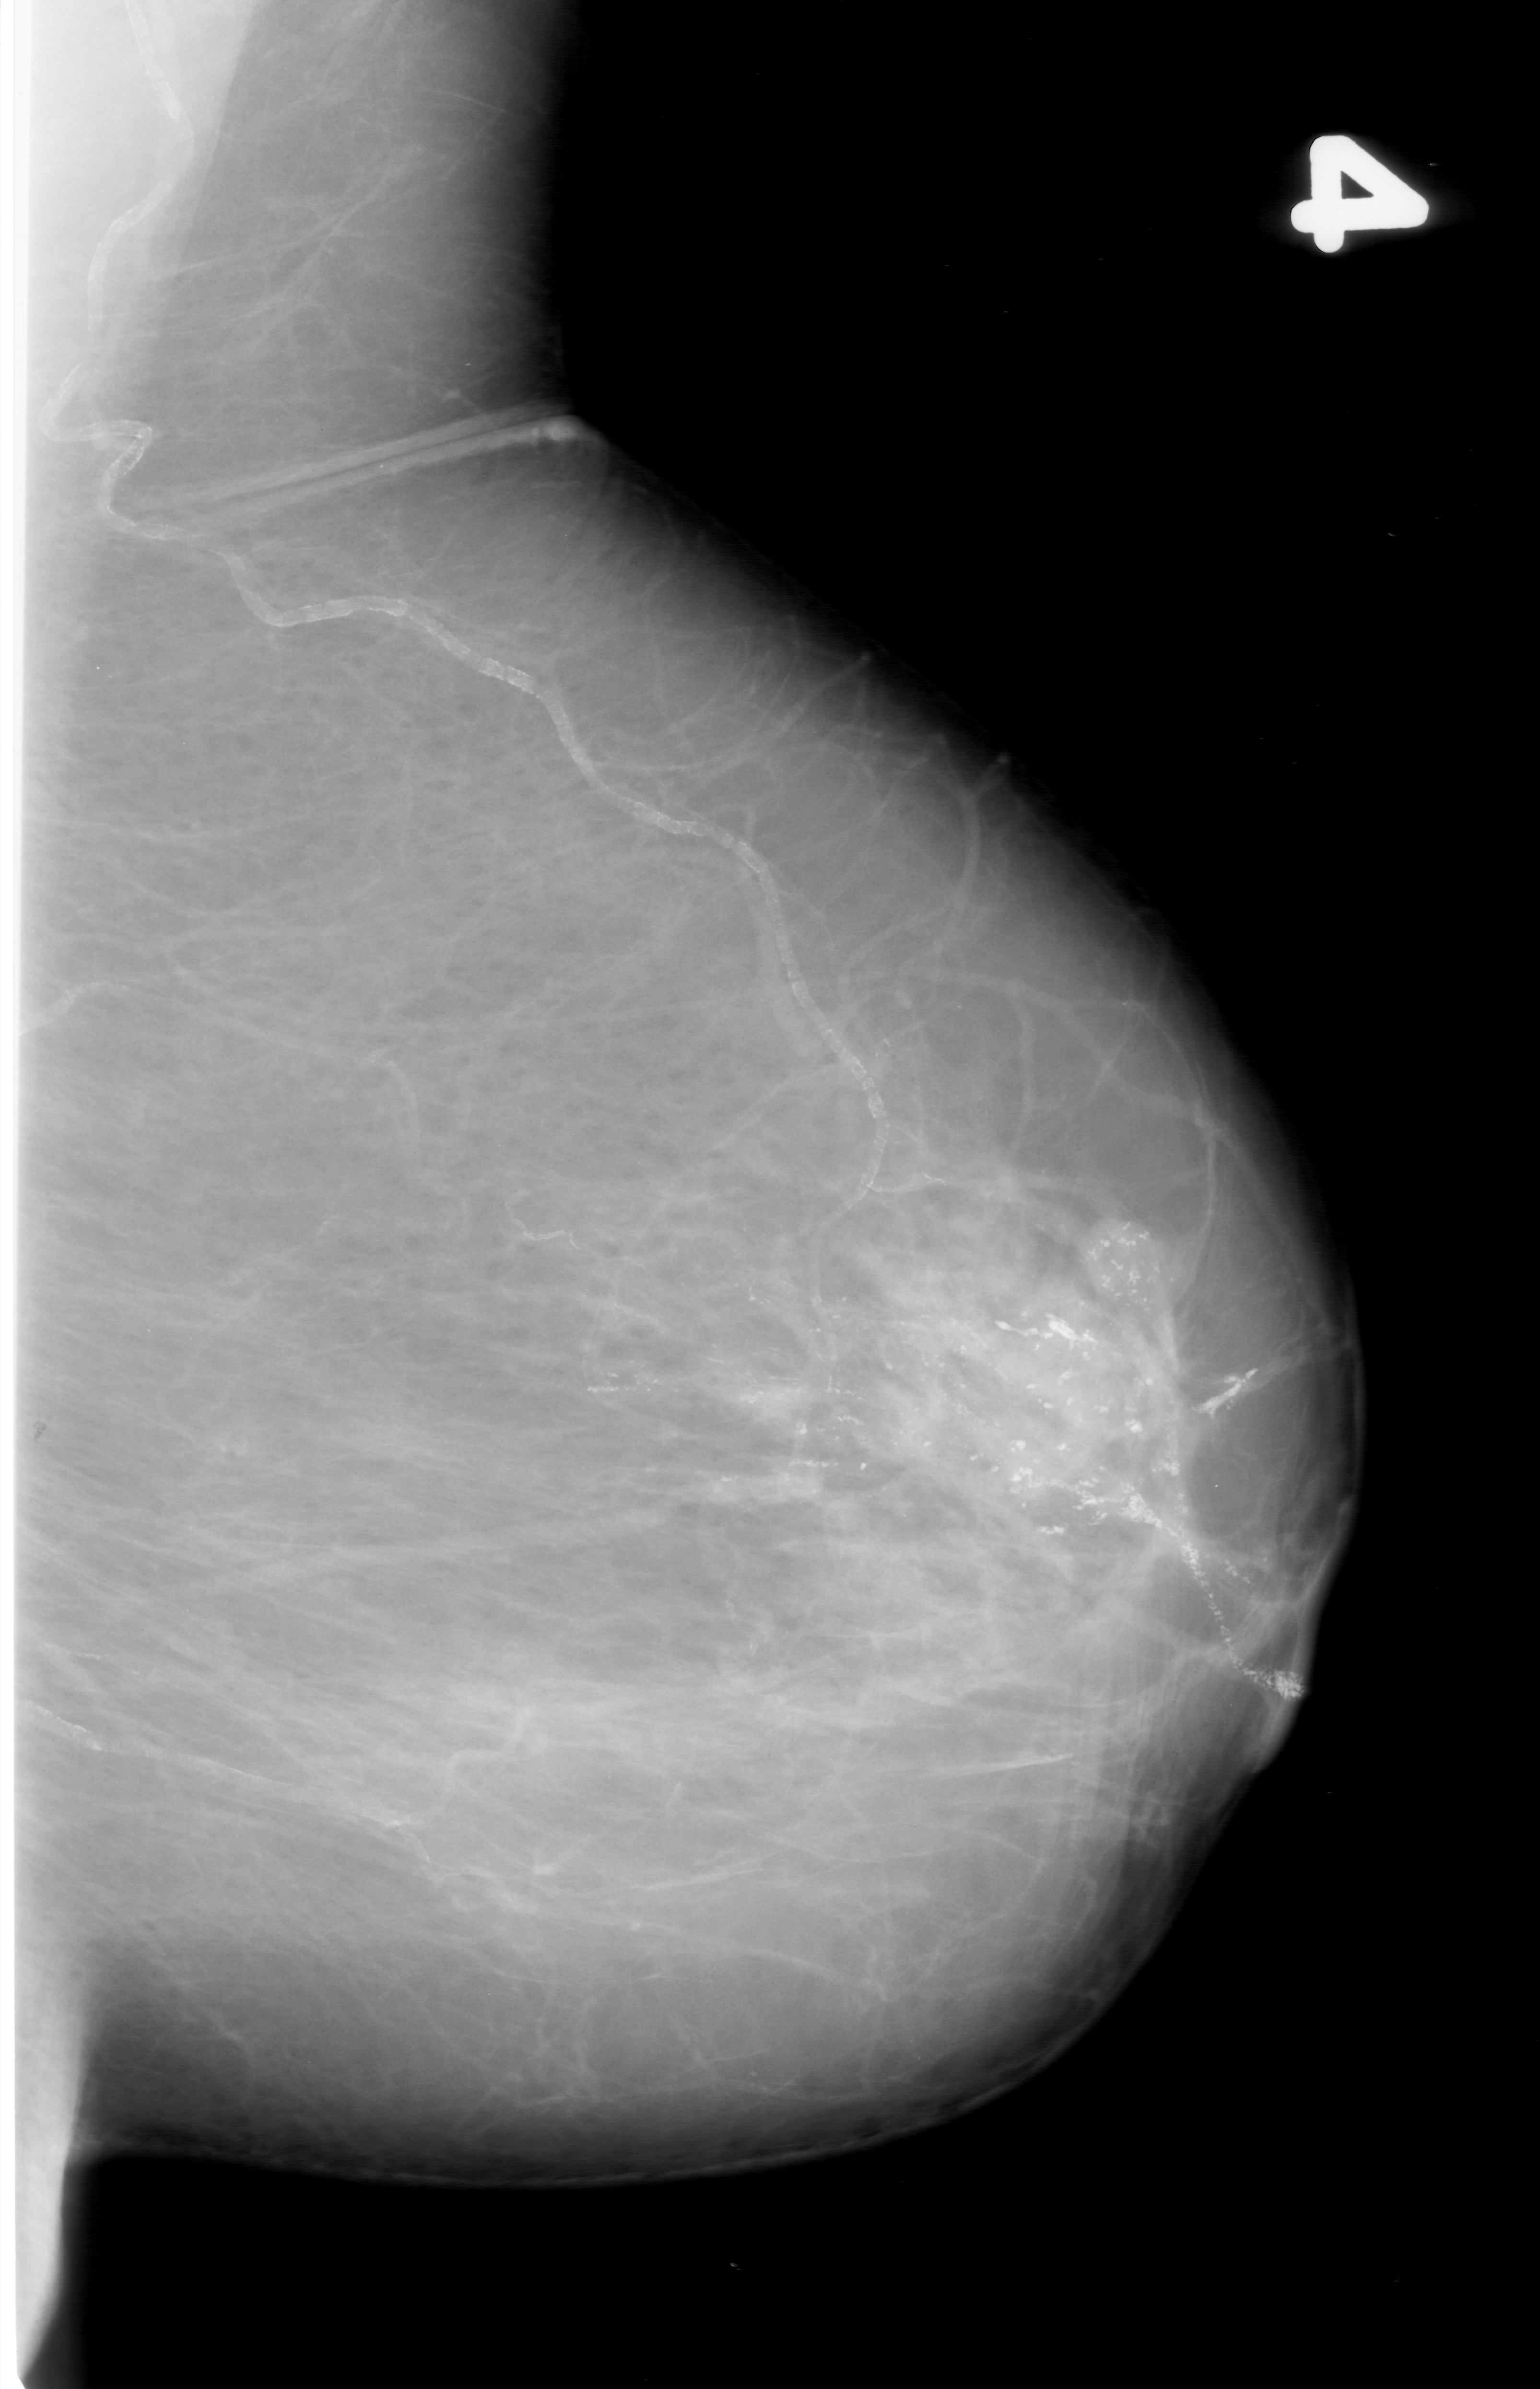
Mammogram (digitized film). Left breast. Mediolateral oblique (MLO) view. Breast composition: almost entirely fatty (BI-RADS density category 1 of 4). 1540 × 2389 image matrix.
Expert-marked regions of interest on this film, with their recorded descriptors:
- calcifications, morphology pleomorphic, distribution linear; BI-RADS assessment category 5; subtlety rating 5 on a 1 (subtle) to 5 (obvious) scale; pathology (as recorded): malignant: bounding box [x1, y1, x2, y2] px = [467, 1054, 1366, 1855]